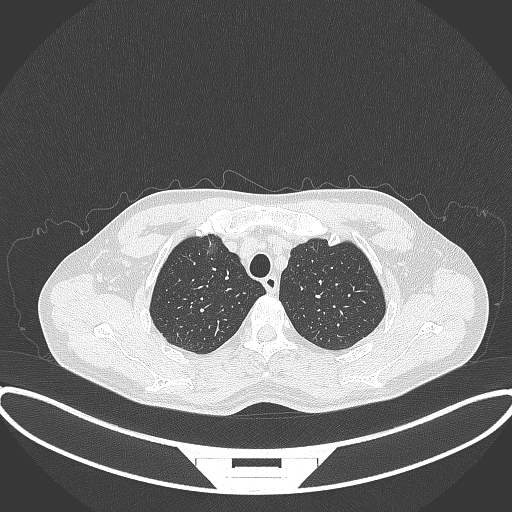
Chest CT, one axial slice. Position 307 of 395 along the scan axis. Reconstruction kernel B70f. 120 kVp. Lung window (W 1500 / L -600 HU). 1 mm slice thickness. 512 × 512 image matrix. Patient: male, 60 years. Case-level facts recorded for this patient, not image findings: clinical TNM (as recorded): T1c N0 M0.
Structures marked on this image (bounding box drawn by a radiologist):
- lung tumour (recorded histology: adenocarcinoma): bounding box (x1, y1, x2, y2) in pixels: (203, 227, 225, 267)